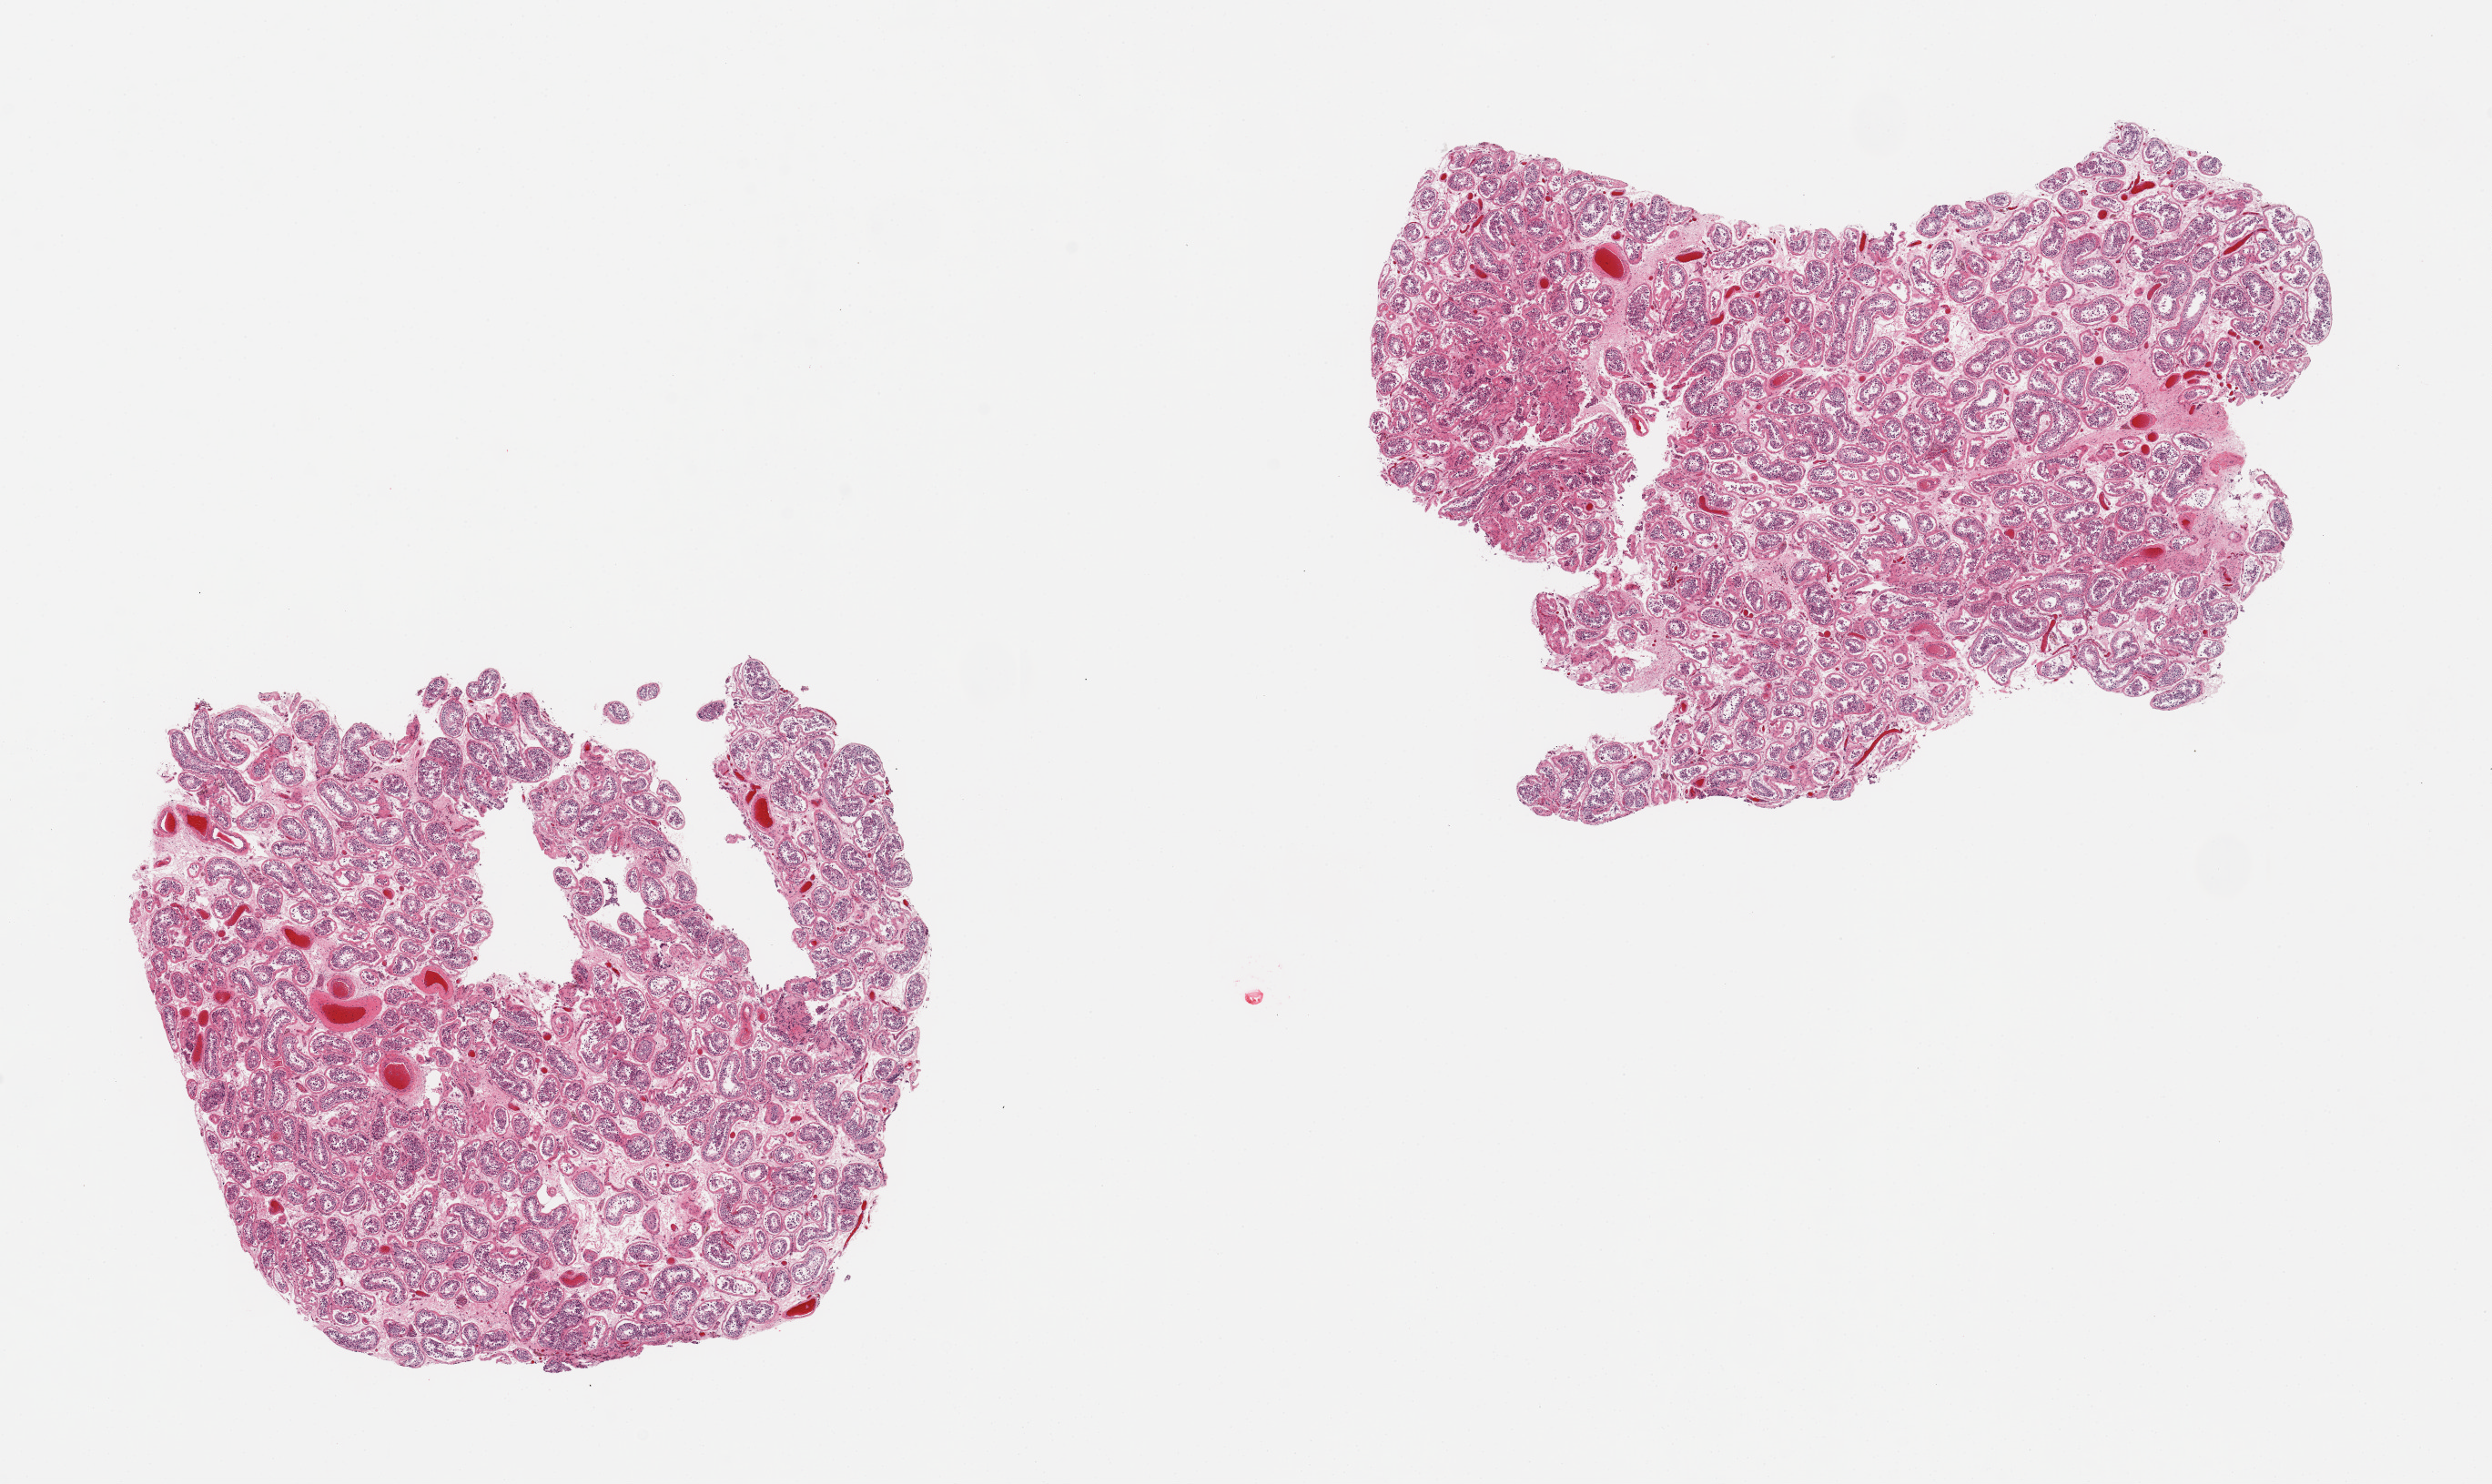
Digitized haematoxylin and eosin-stained section, brightfield, low-resolution overview of the scanned area, about 21.7 x 12.9 mm, PAXgene-fixed paraffin-embedded (PFPE) section, section of testis (target tissue), donor tissue sample. Donor: male.
* review note (as recorded): 2 pieces; reduced spermatogenesis